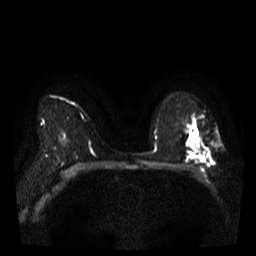
Breast MRI, one axial slice; position 25 of 38 along the scan axis; diffusion-weighted series; image 2 of 4 stored at this slice position (different b-values; order by instance number); 3 T; 5 mm slice thickness; 256 × 256 image matrix. Female patient.
Annotated regions visible in this slice (outlined manually by an expert reader):
- tumour on diffusion-weighted imaging: box from (x=203, y=148) to (x=209, y=153) px